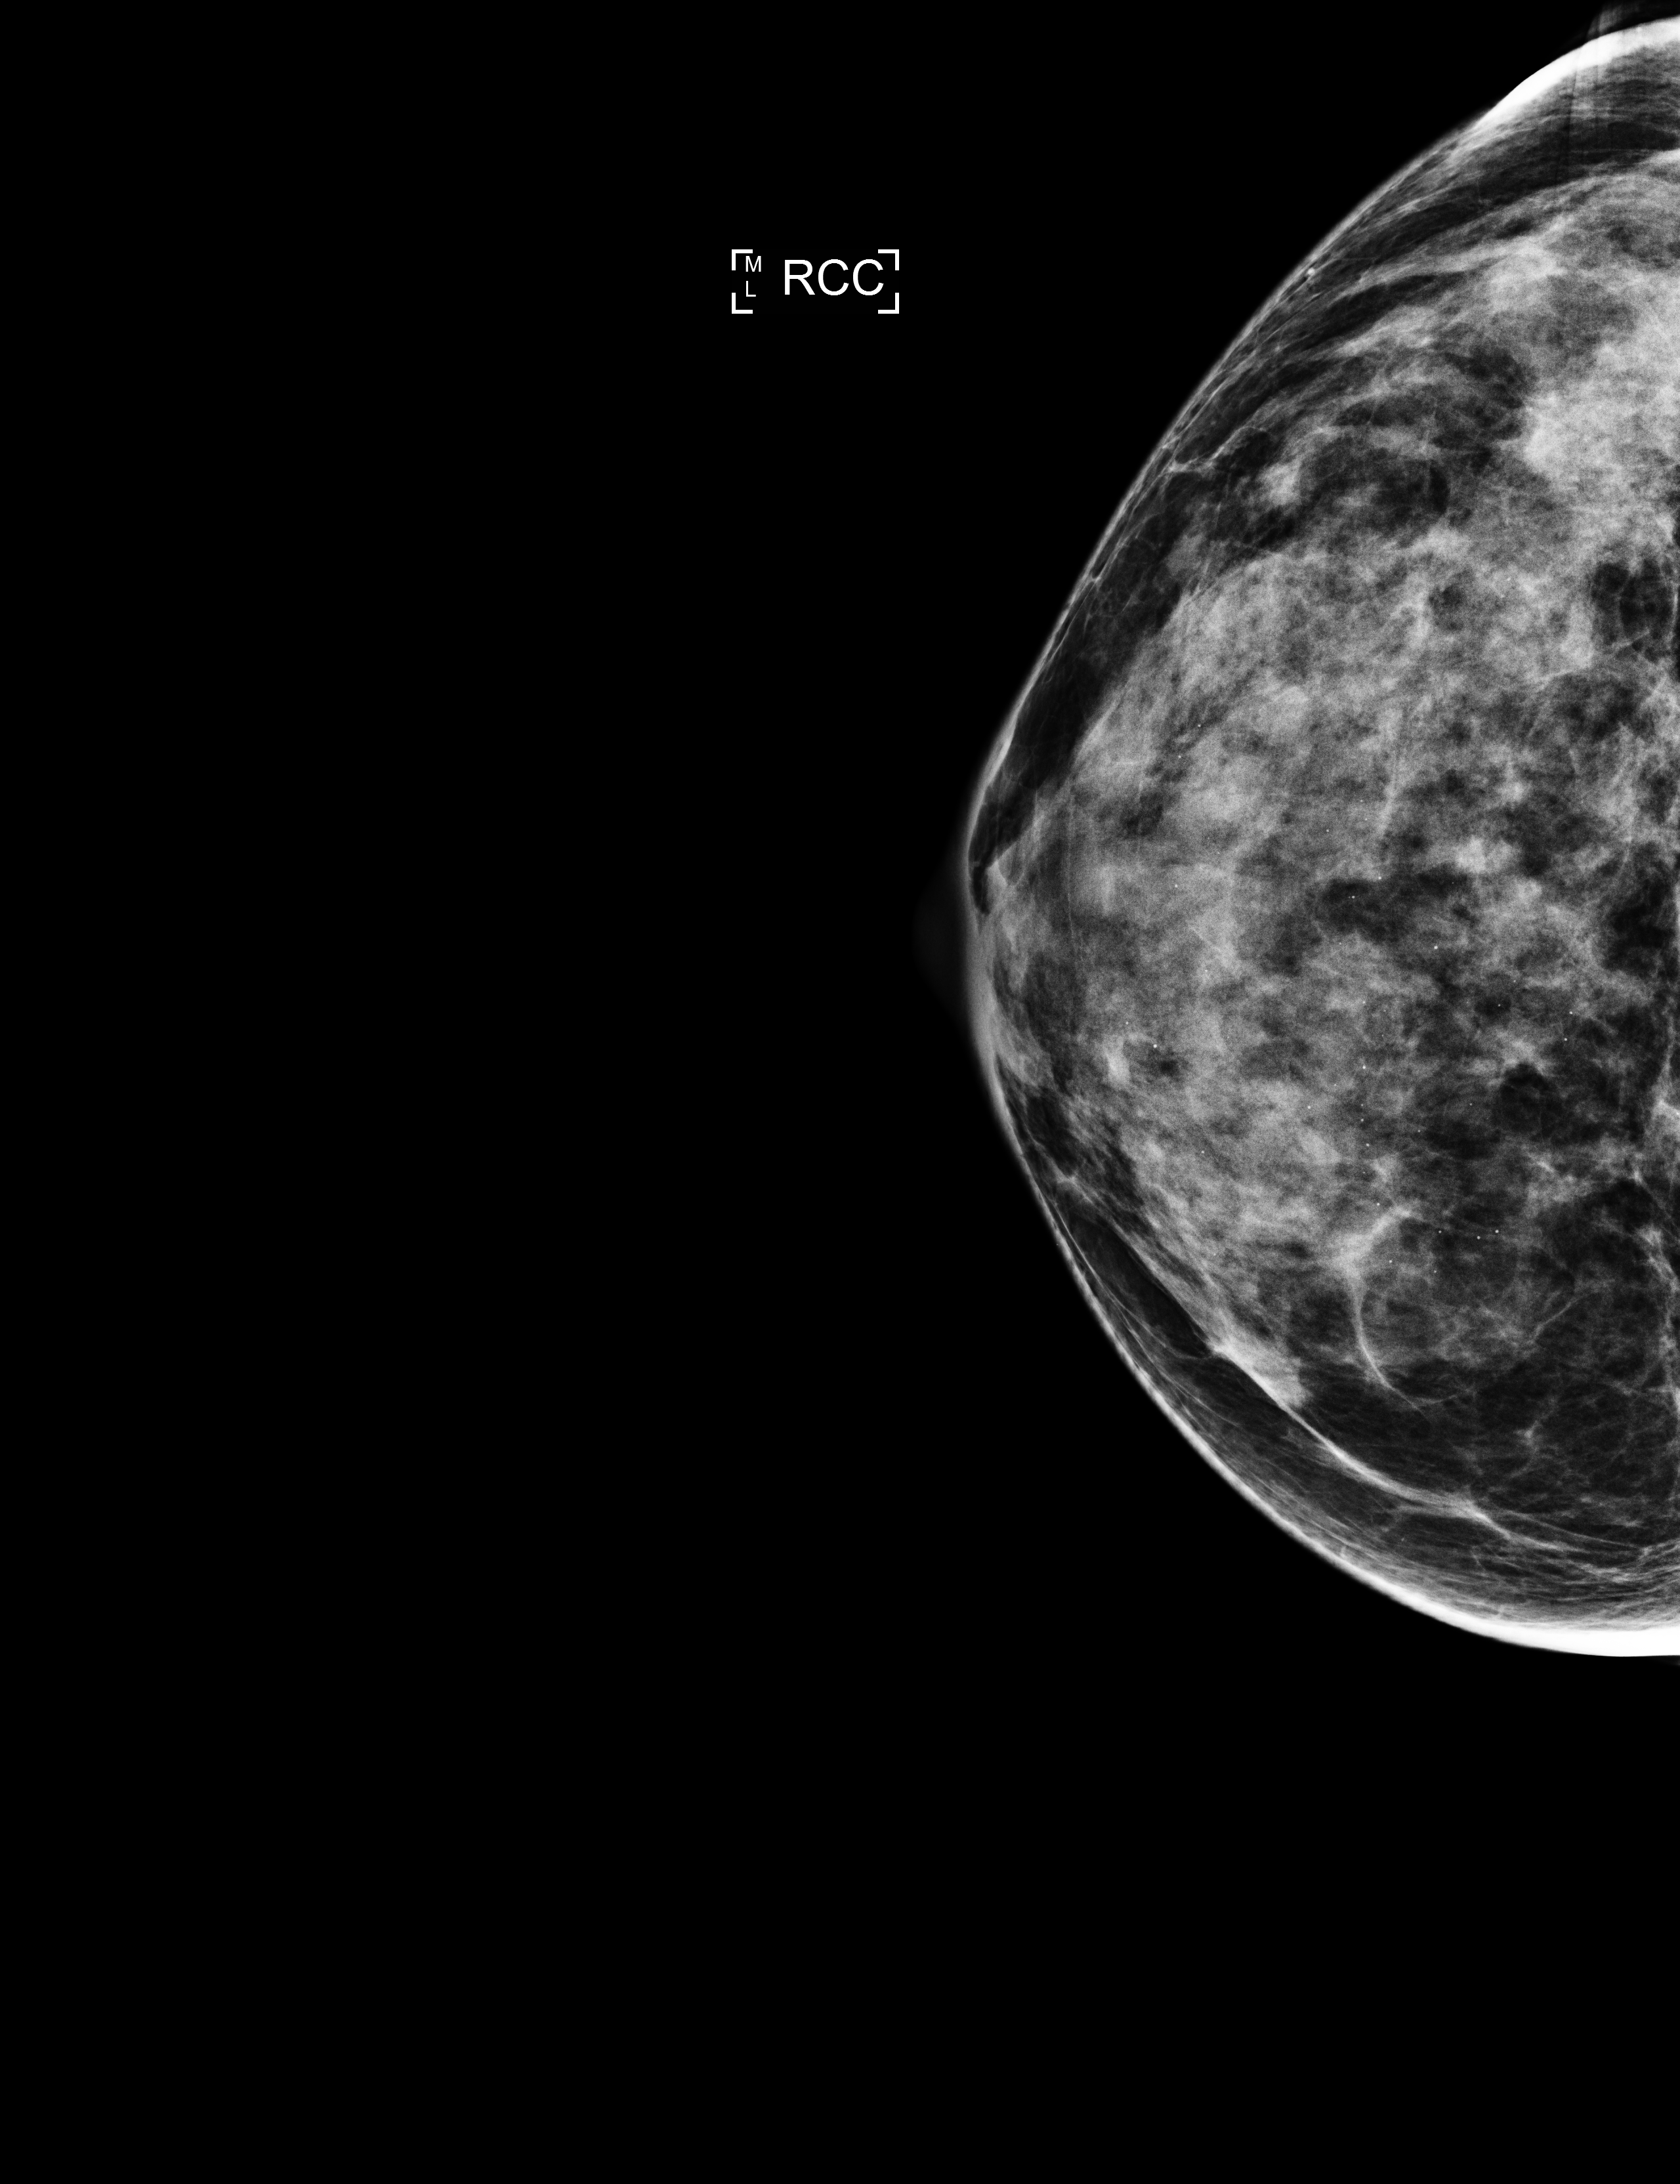
Annual screening mammography examination; compressed breast thickness 51 mm. Patient aged 47 years (female).
Image type: full-field digital mammogram. Breast: right. Projection: cranio-caudal projection.